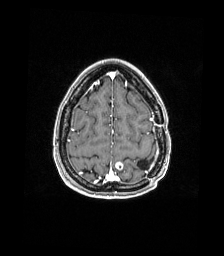
Brain MRI from a brain-tumour surgery series, one axial slice. Slice 42 of 176 in the series (ordered by position). T1-weighted post-contrast. 224 × 256 image matrix, field of view 224 × 256 mm. Case-level facts recorded for this patient, not image findings: histopathology: Atypical meningioma; WHO grade: 2.
Annotated regions visible in this slice (outlined manually by an expert reader):
- previous resection cavity: bounding box [x1, y1, x2, y2] px = [137, 160, 149, 169]
- tumour: [115, 162, 124, 170]